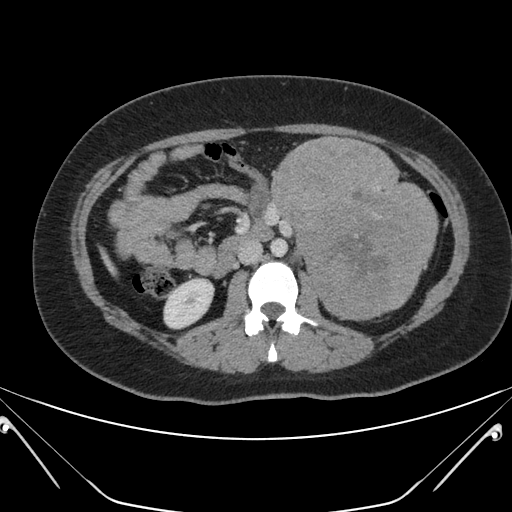
Contrast-enhanced abdominal CT, one axial slice; position 103 of 168 along the scan axis; intravenous contrast given; soft-tissue window (W 400 / L 40 HU); 512 × 512 image matrix, field of view 394 × 394 mm. Female patient, age 26 years. Case-level facts recorded for this patient, not image findings: diagnosis: adrenocortical carcinoma; tumour side: left adrenal; tumour size at pathology: 28 cm; Ki-67 index: 20 %; stage (as recorded): 2.
Structures marked on this image (semi-automatic segmentation, software-assisted and operator-edited):
- mass: box from (x=274, y=136) to (x=437, y=319) px